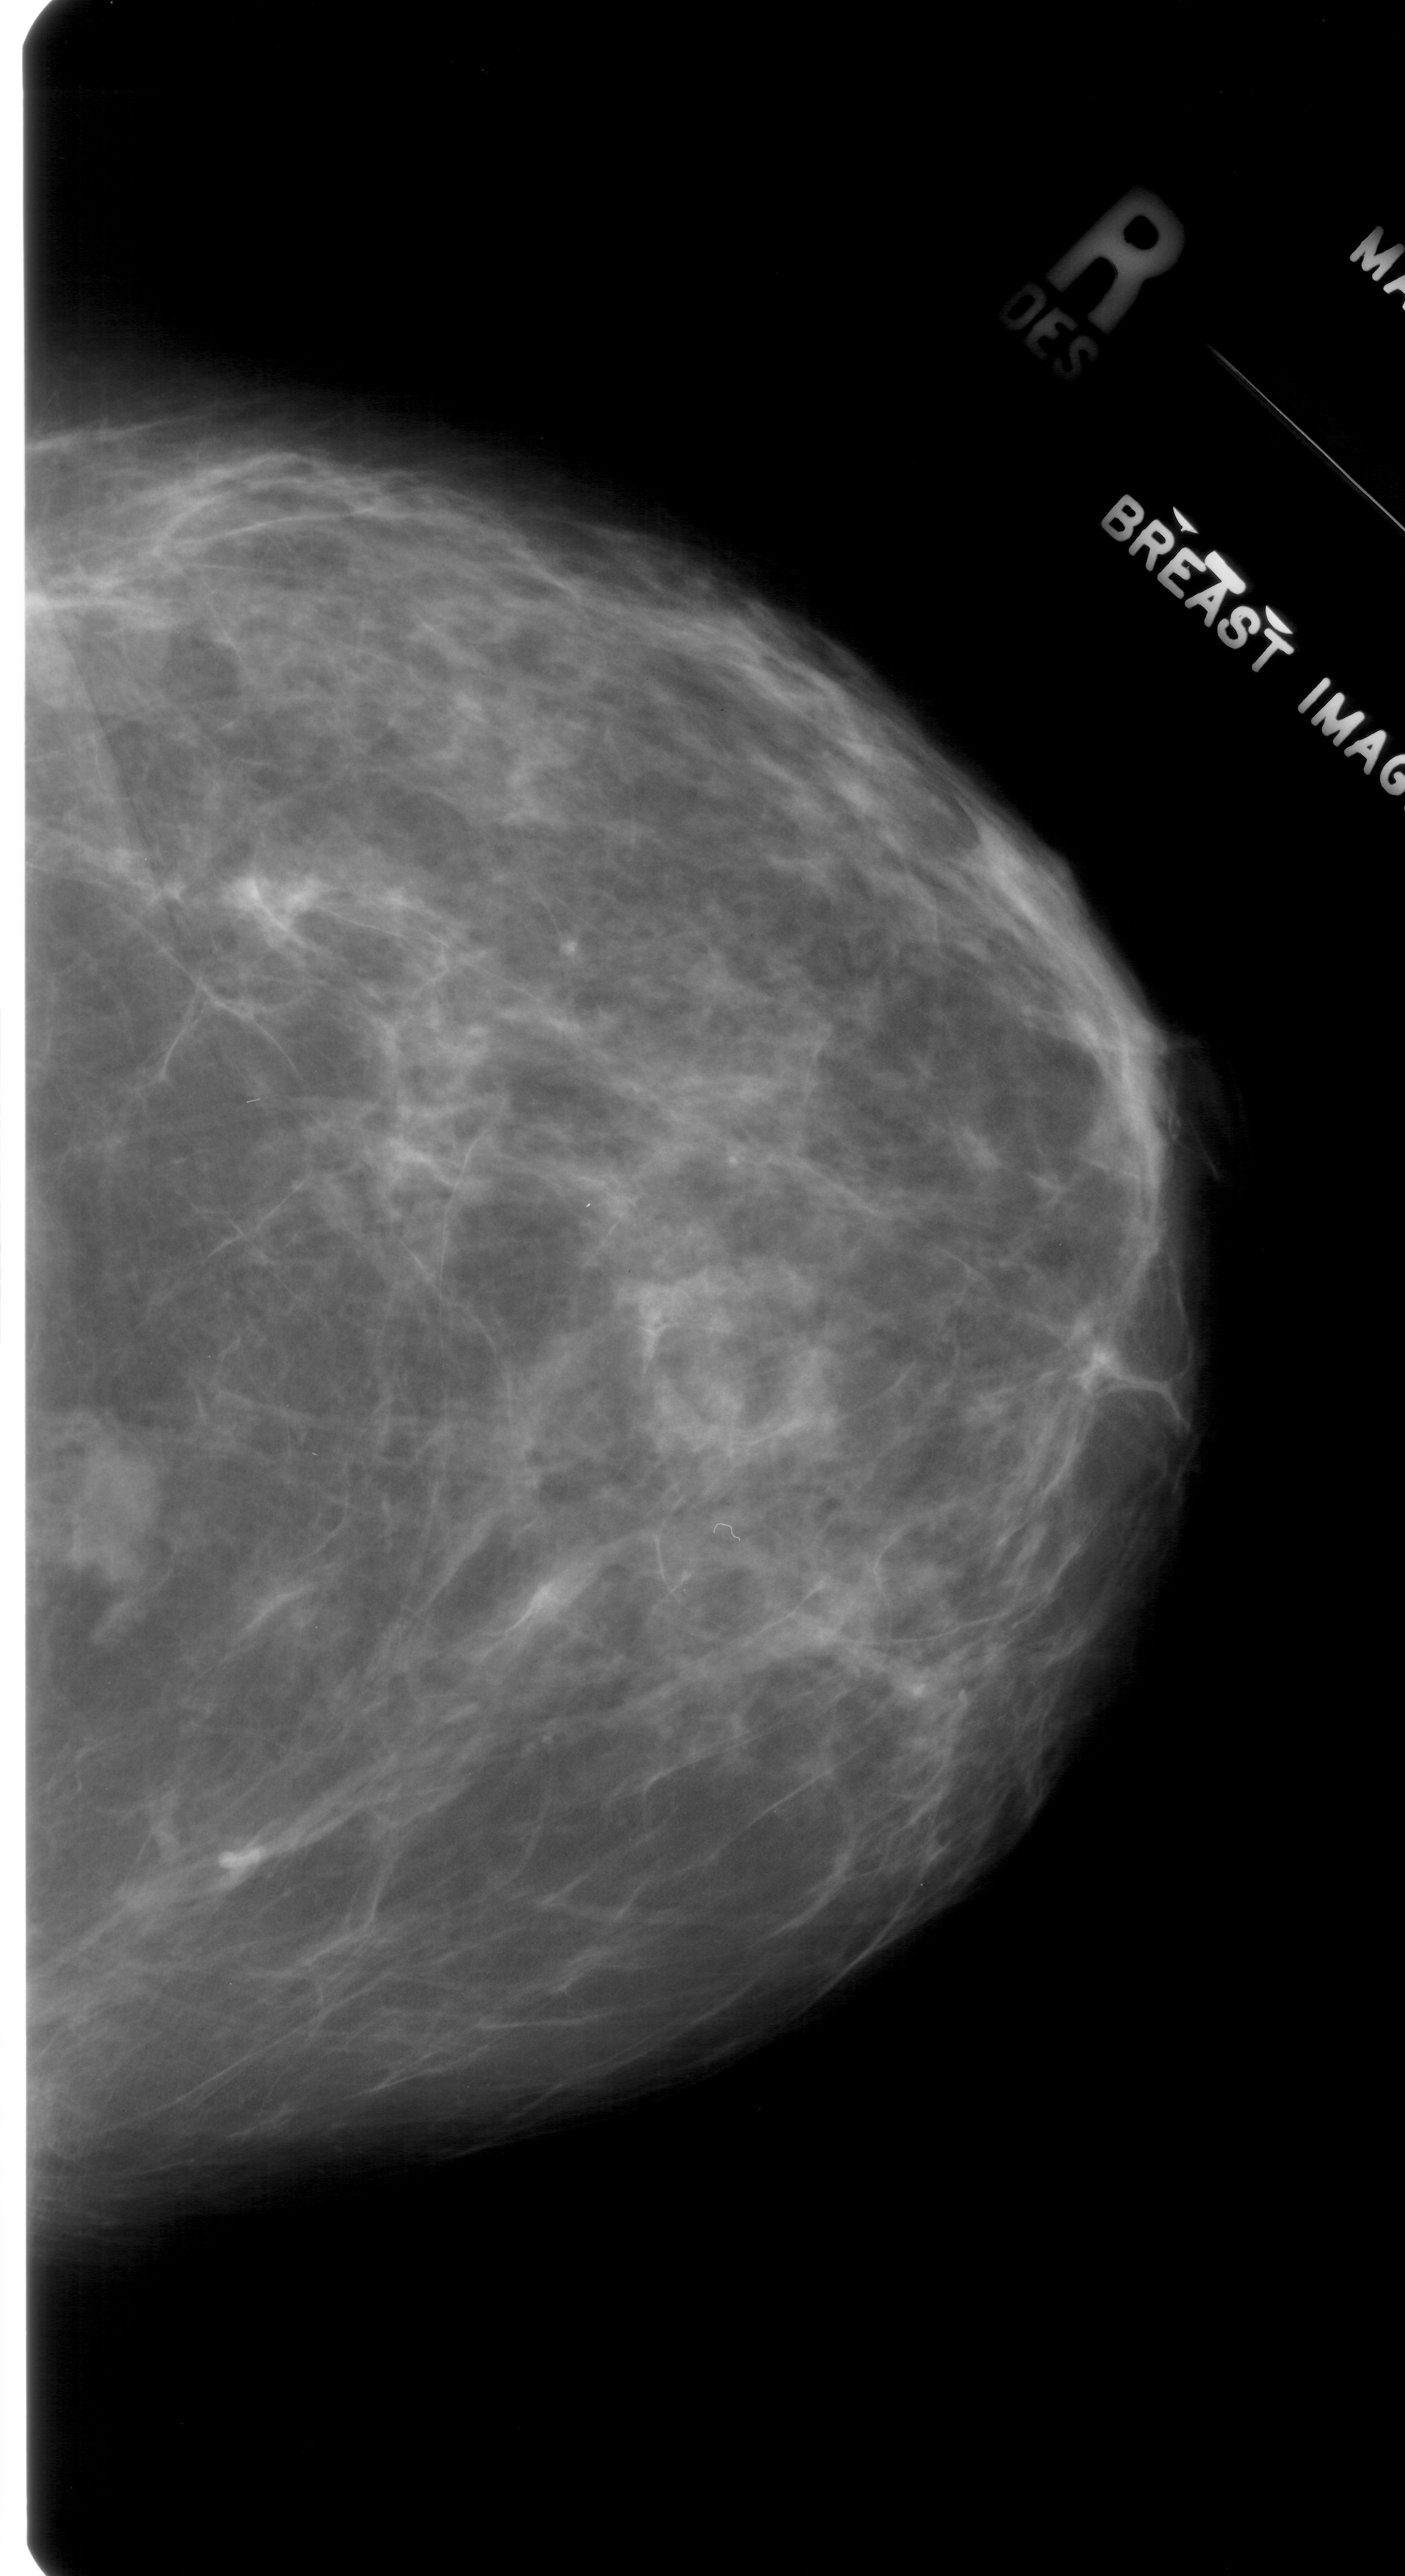
Mammogram (digitized film), right breast, CC view, BI-RADS breast density category 3 (scale 1–4).
Finding: mass, shape irregular, margins ill defined; BI-RADS assessment category 4; pathology (as recorded): benign.